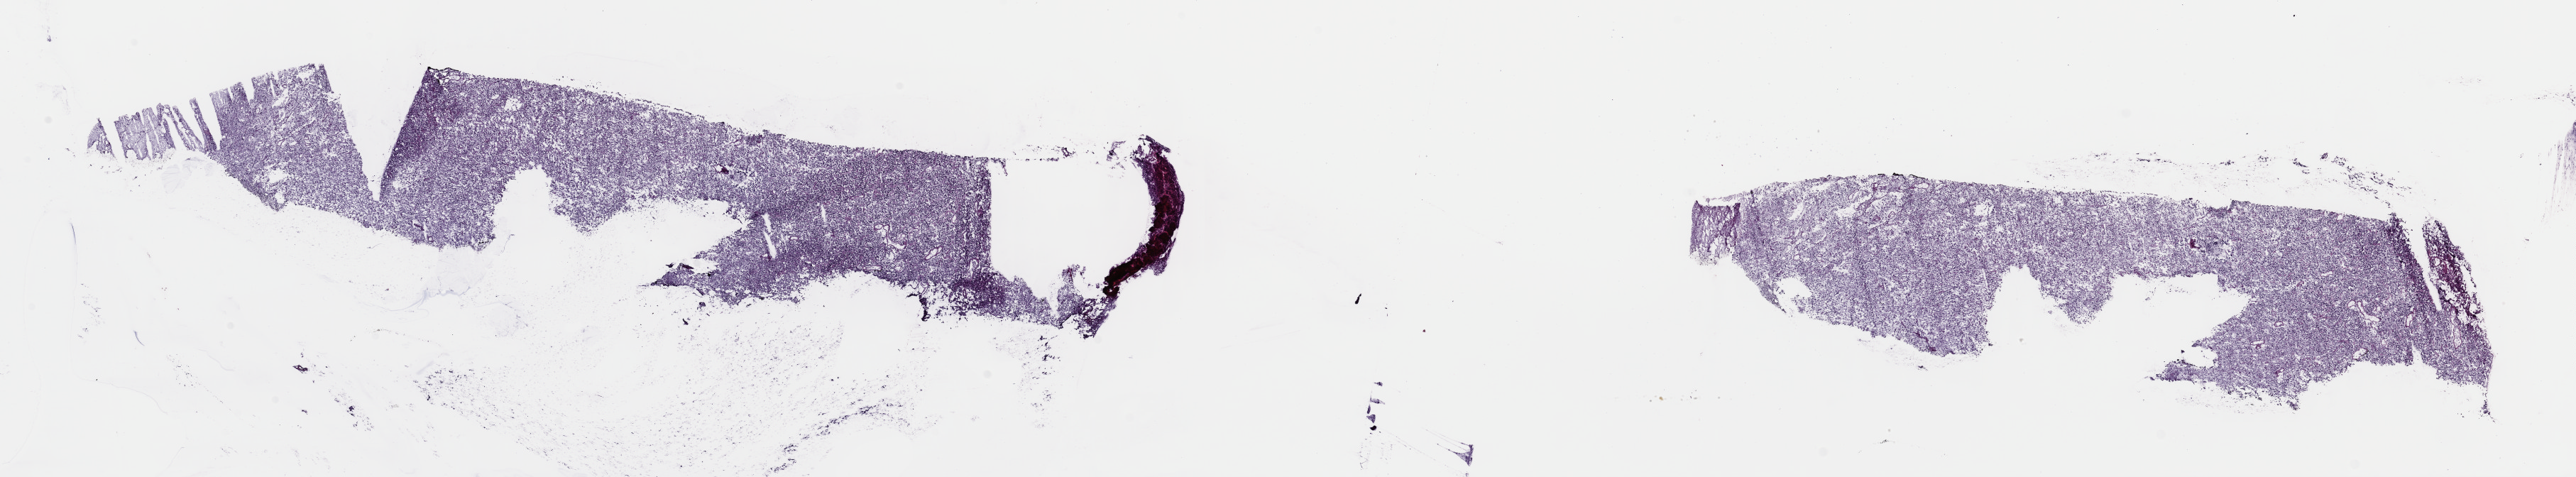
Whole-slide histology image, H&E — a low-resolution overview of the entire scanned area, about 28.7 x 5.3 mm (acquisition: 40x scan). Frozen section from the top of the tissue portion. Primary tumour sample from the brain. Male, age 68 years at initial diagnosis. Histologic grade: G3 (poorly differentiated). Slide review estimates, as recorded: tumour cells 85%, tumour nuclei 90%, normal cells 5%, stromal cells 10%, necrosis 0%. Infiltration values recorded for this section: lymphocyte infiltration 0%, monocyte infiltration 0%, neutrophil infiltration 0%.
Pathologic diagnosis: Oligodendroglioma, anaplastic (cerebrum).